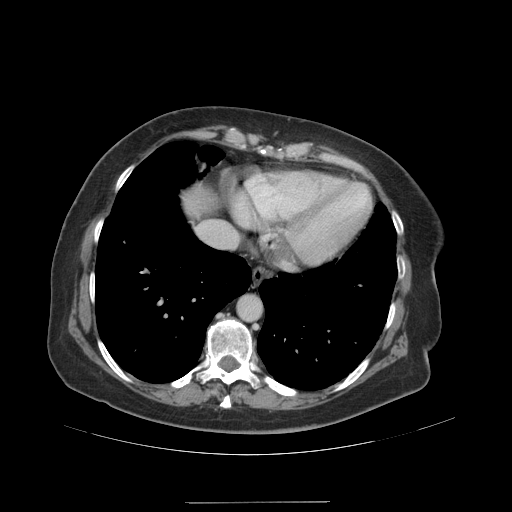
Contrast-enhanced abdominal CT (liver protocol), one axial slice; 140 kVp; soft-tissue window (W 400 / L 40 HU); 2.5 mm slice thickness; 512 × 512 image matrix, field of view 440 × 440 mm. Case-level facts recorded for this patient, not image findings: diagnosis: hepatocellular carcinoma (patient treated with transarterial chemoembolisation; whether this scan precedes or follows treatment is not stated here); TNM stage (as recorded): Stage-IVA; Child-Pugh class: A; tumour nodularity: multinodular.
Structures marked on this image (semi-automatic segmentation, software-assisted and operator-edited):
- abdominal aorta: box from (x=238, y=296) to (x=261, y=320) px
- liver parenchyma outside the tumour (the mass and vessels are separate outlines, so this box may not span the whole liver): (x=184, y=192)–(x=210, y=217)